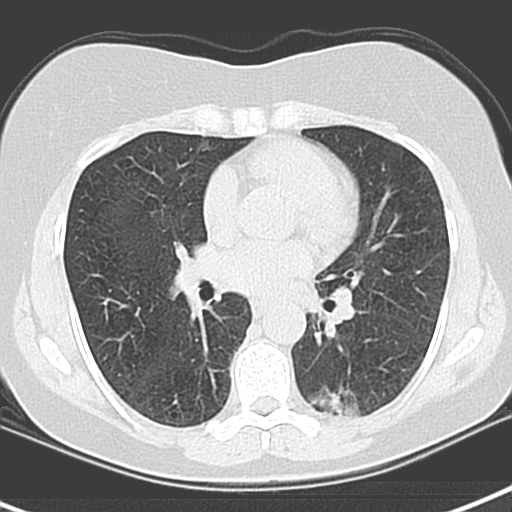
Axial slice from a low-dose chest CT screening exam. First (baseline) screen. Lung window (W 1500 / L -600 HU). Standard (soft-tissue) reconstruction kernel (B). 120 kVp. Slice 70 of 129 in the series. 512 × 512 image matrix. Female, age 55 years at enrolment. Current smoker at enrolment.
Expert reader's lesion annotation, bounding box (x1, y1, x2, y2) in pixels: (309, 374, 386, 424). The screening reader recorded 3 non-calcified nodules or masses ≥4 mm on this exam; which of them this box marks is not recorded. Participant outcome: lung cancer diagnosed 1063 days after this screen — adenocarcinoma with mixed subtypes, left lower lobe, poorly differentiated (G3), stage IA (AJCC 6th edition), 21 mm at pathology.